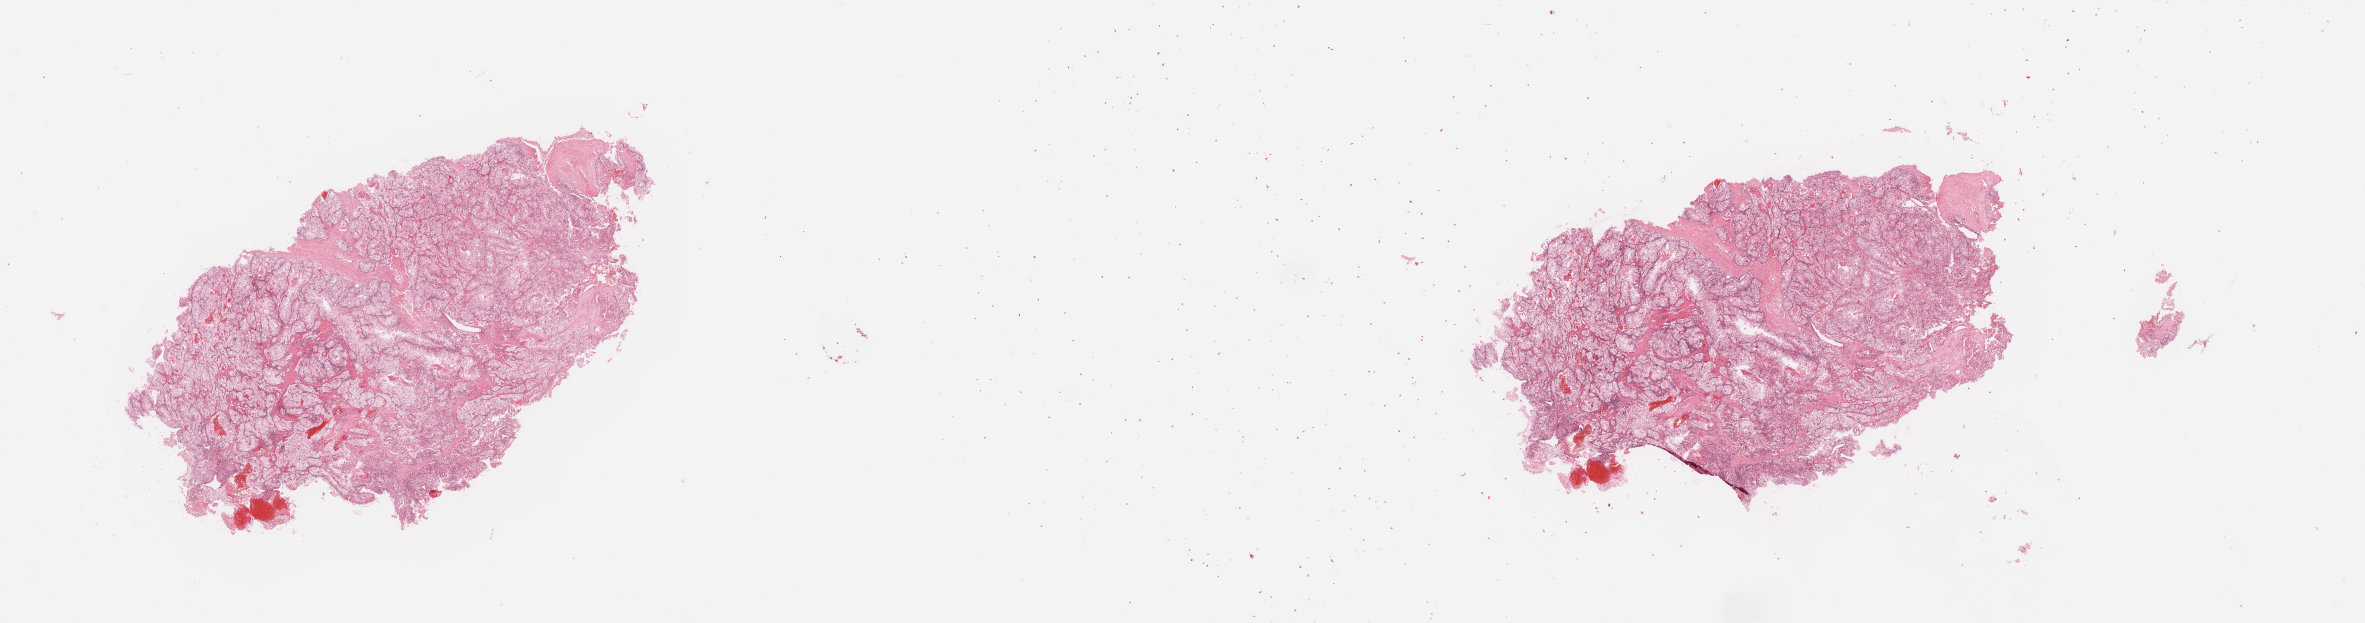
Digitized Hematoxylin and eosin (H&E) stained tissue section (whole slide), shown as a low-resolution overview of the whole scanned area (about 37.4 x 9.9 mm, slide scanned at 20x); kidney, tumour tissue. Patient: male, age 54 years. Histologic grade: G2 (moderately differentiated).
AJCC pathologic stage: I. Diagnosis: Renal cell carcinoma, NOS. Primary tumour site (as recorded): middle.